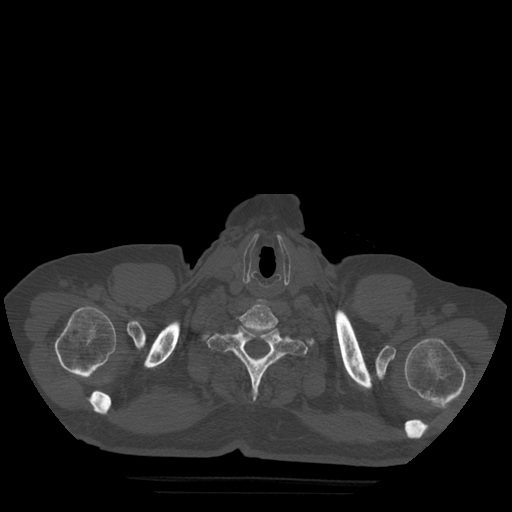
CT including the spine, one axial slice; position 443 of 522 along the scan axis; bone window (W 1800 / L 400 HU); 1.25 mm slice thickness; 512 × 512 image matrix. Patient age 72 years. Case-level facts recorded for this patient, not image findings: primary cancer: prostate.
Outlined on this slice (semi-automatically segmented with operator editing):
- T1 vertebra: bounding box (x1, y1, x2, y2) in pixels: (207, 326, 308, 401)